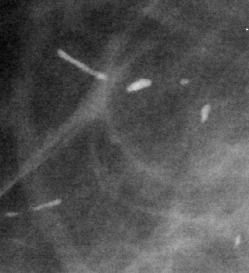
Region of interest cut from a scanned film mammogram (one marked finding), right breast, CC view, BI-RADS breast density category 1 (scale 1–4).
Calcifications, distribution regional; BI-RADS assessment category 2; benign; no additional work-up was recommended (benign without callback).